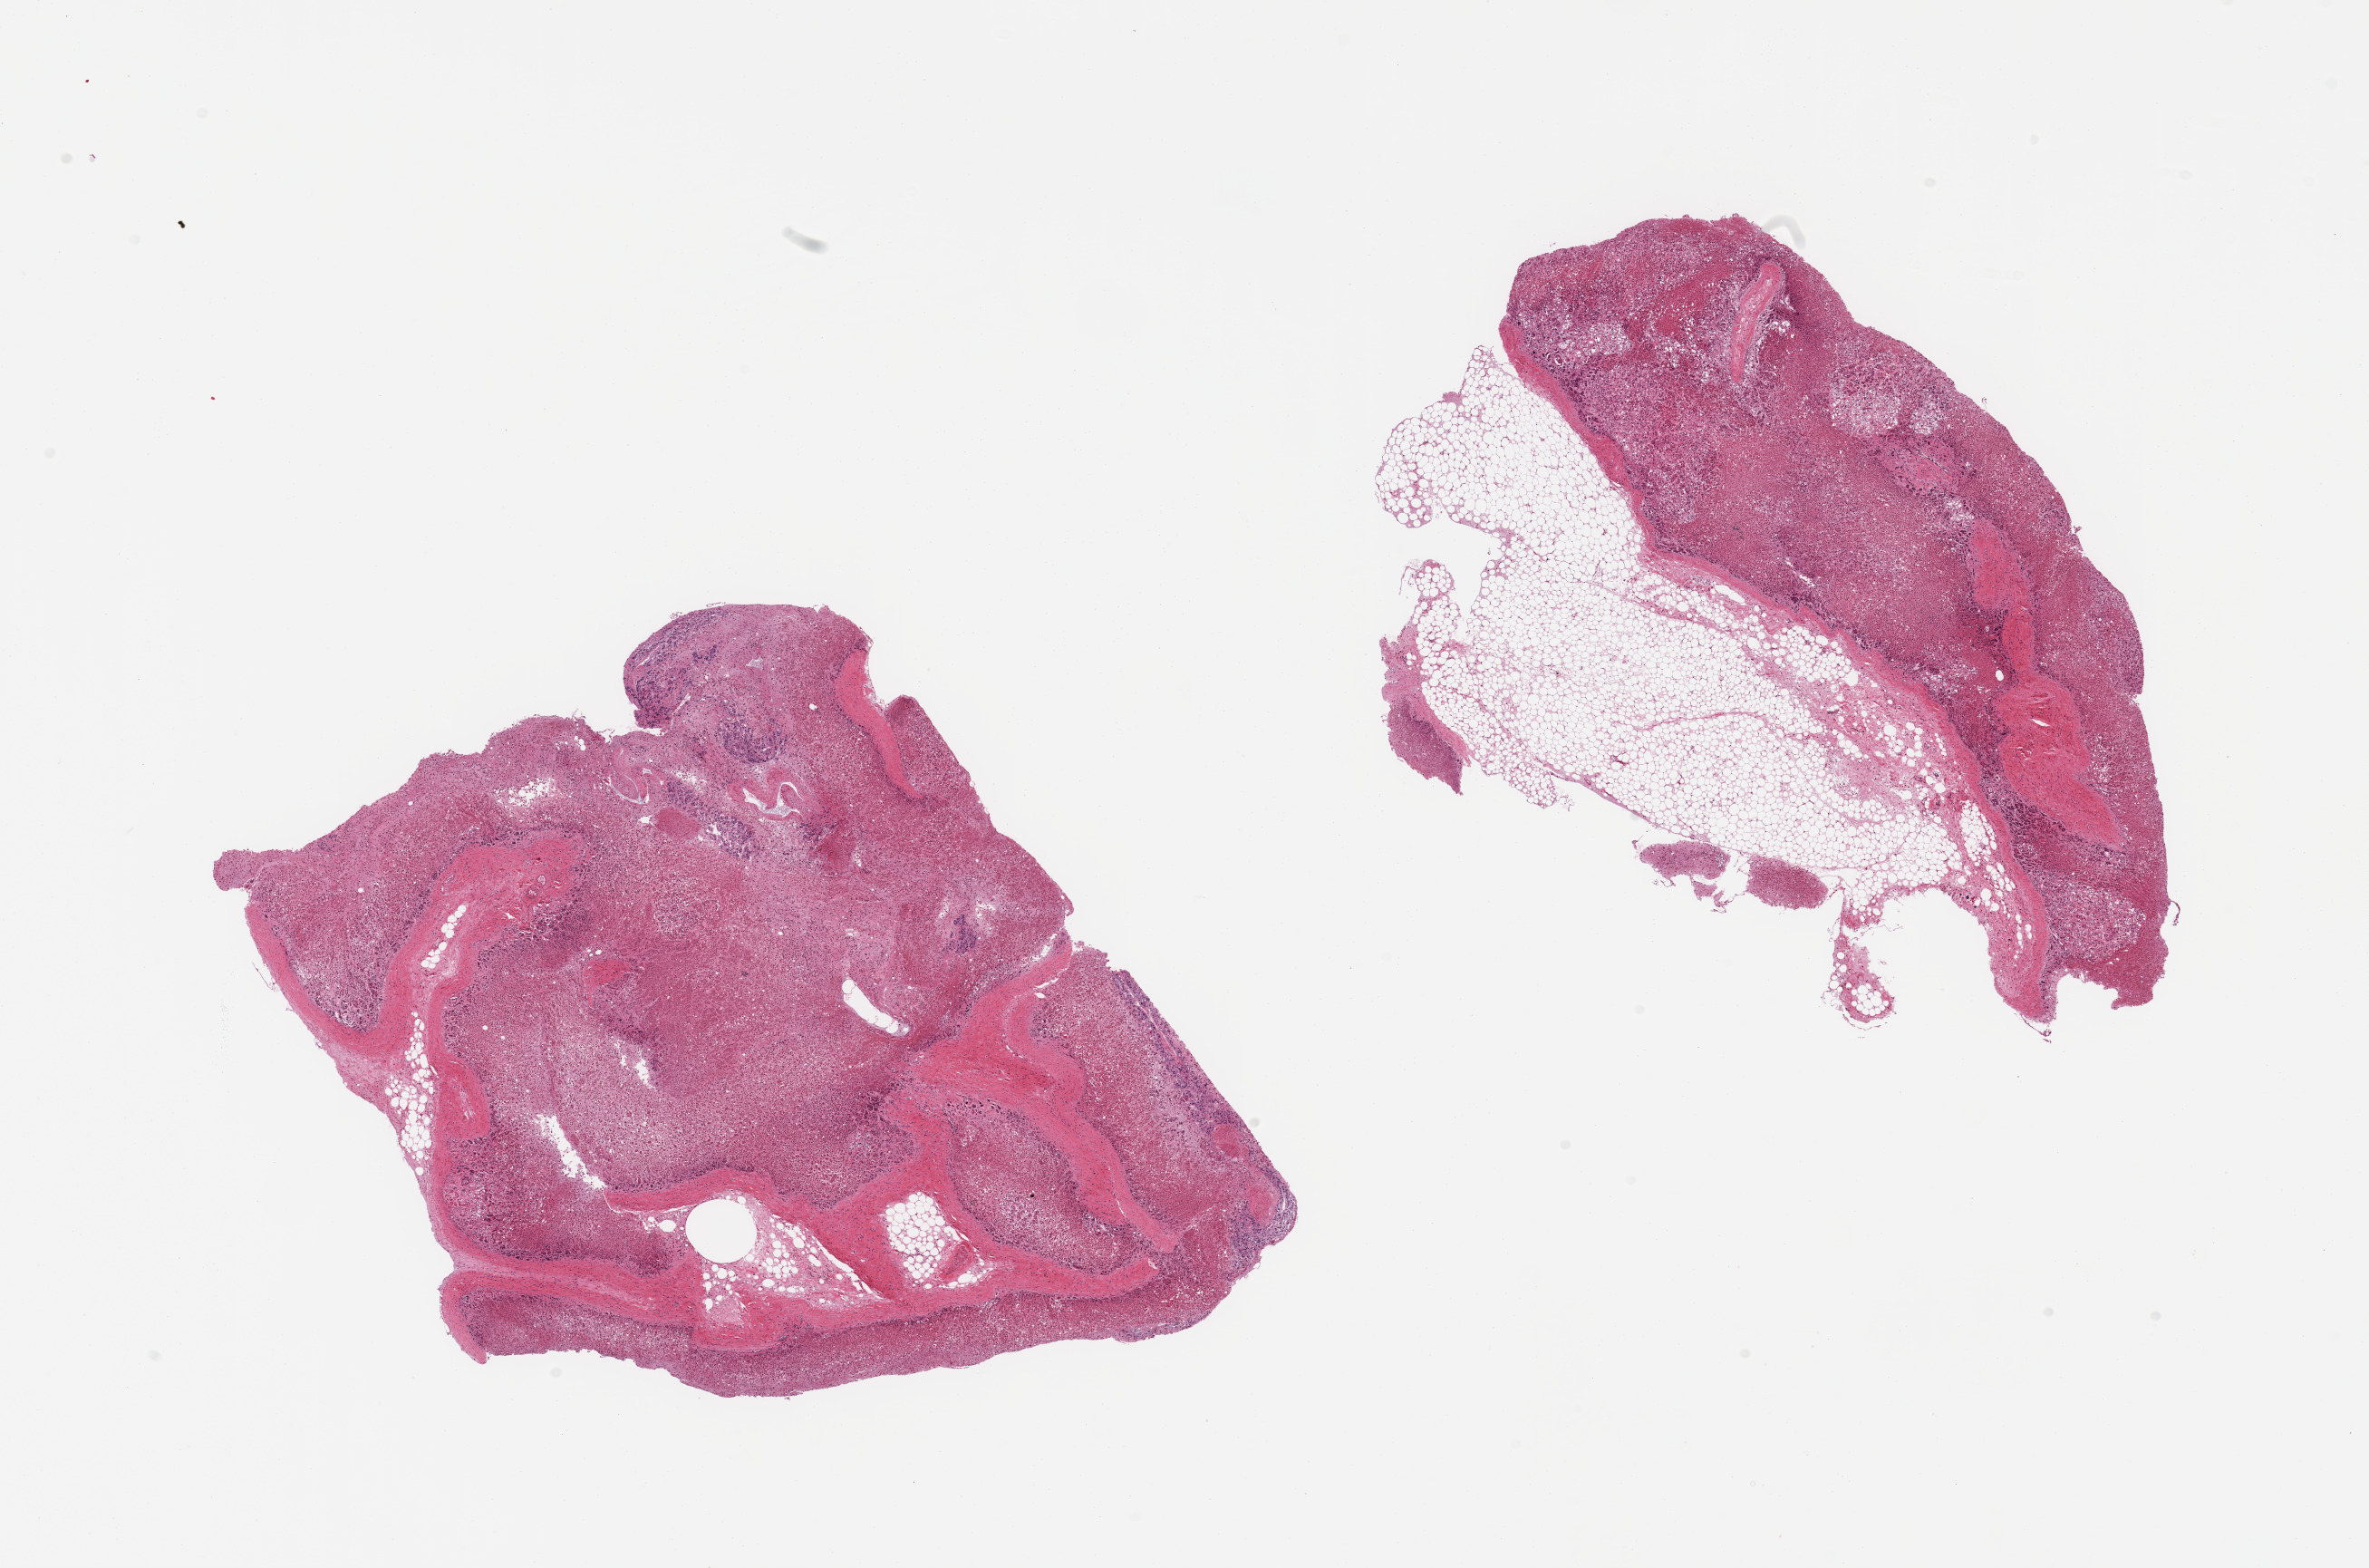
Digitized H&E-stained section — whole scanned area (about 20.7 x 13.7 mm) shown as a low-resolution overview; PAXgene-fixed, paraffin-embedded tissue; section of adrenal gland (target tissue); tissue donor sample. Donor sex: male.
* review note (as recorded): 2 pieces; cortex, advanced autolysis,~30% adherent fat